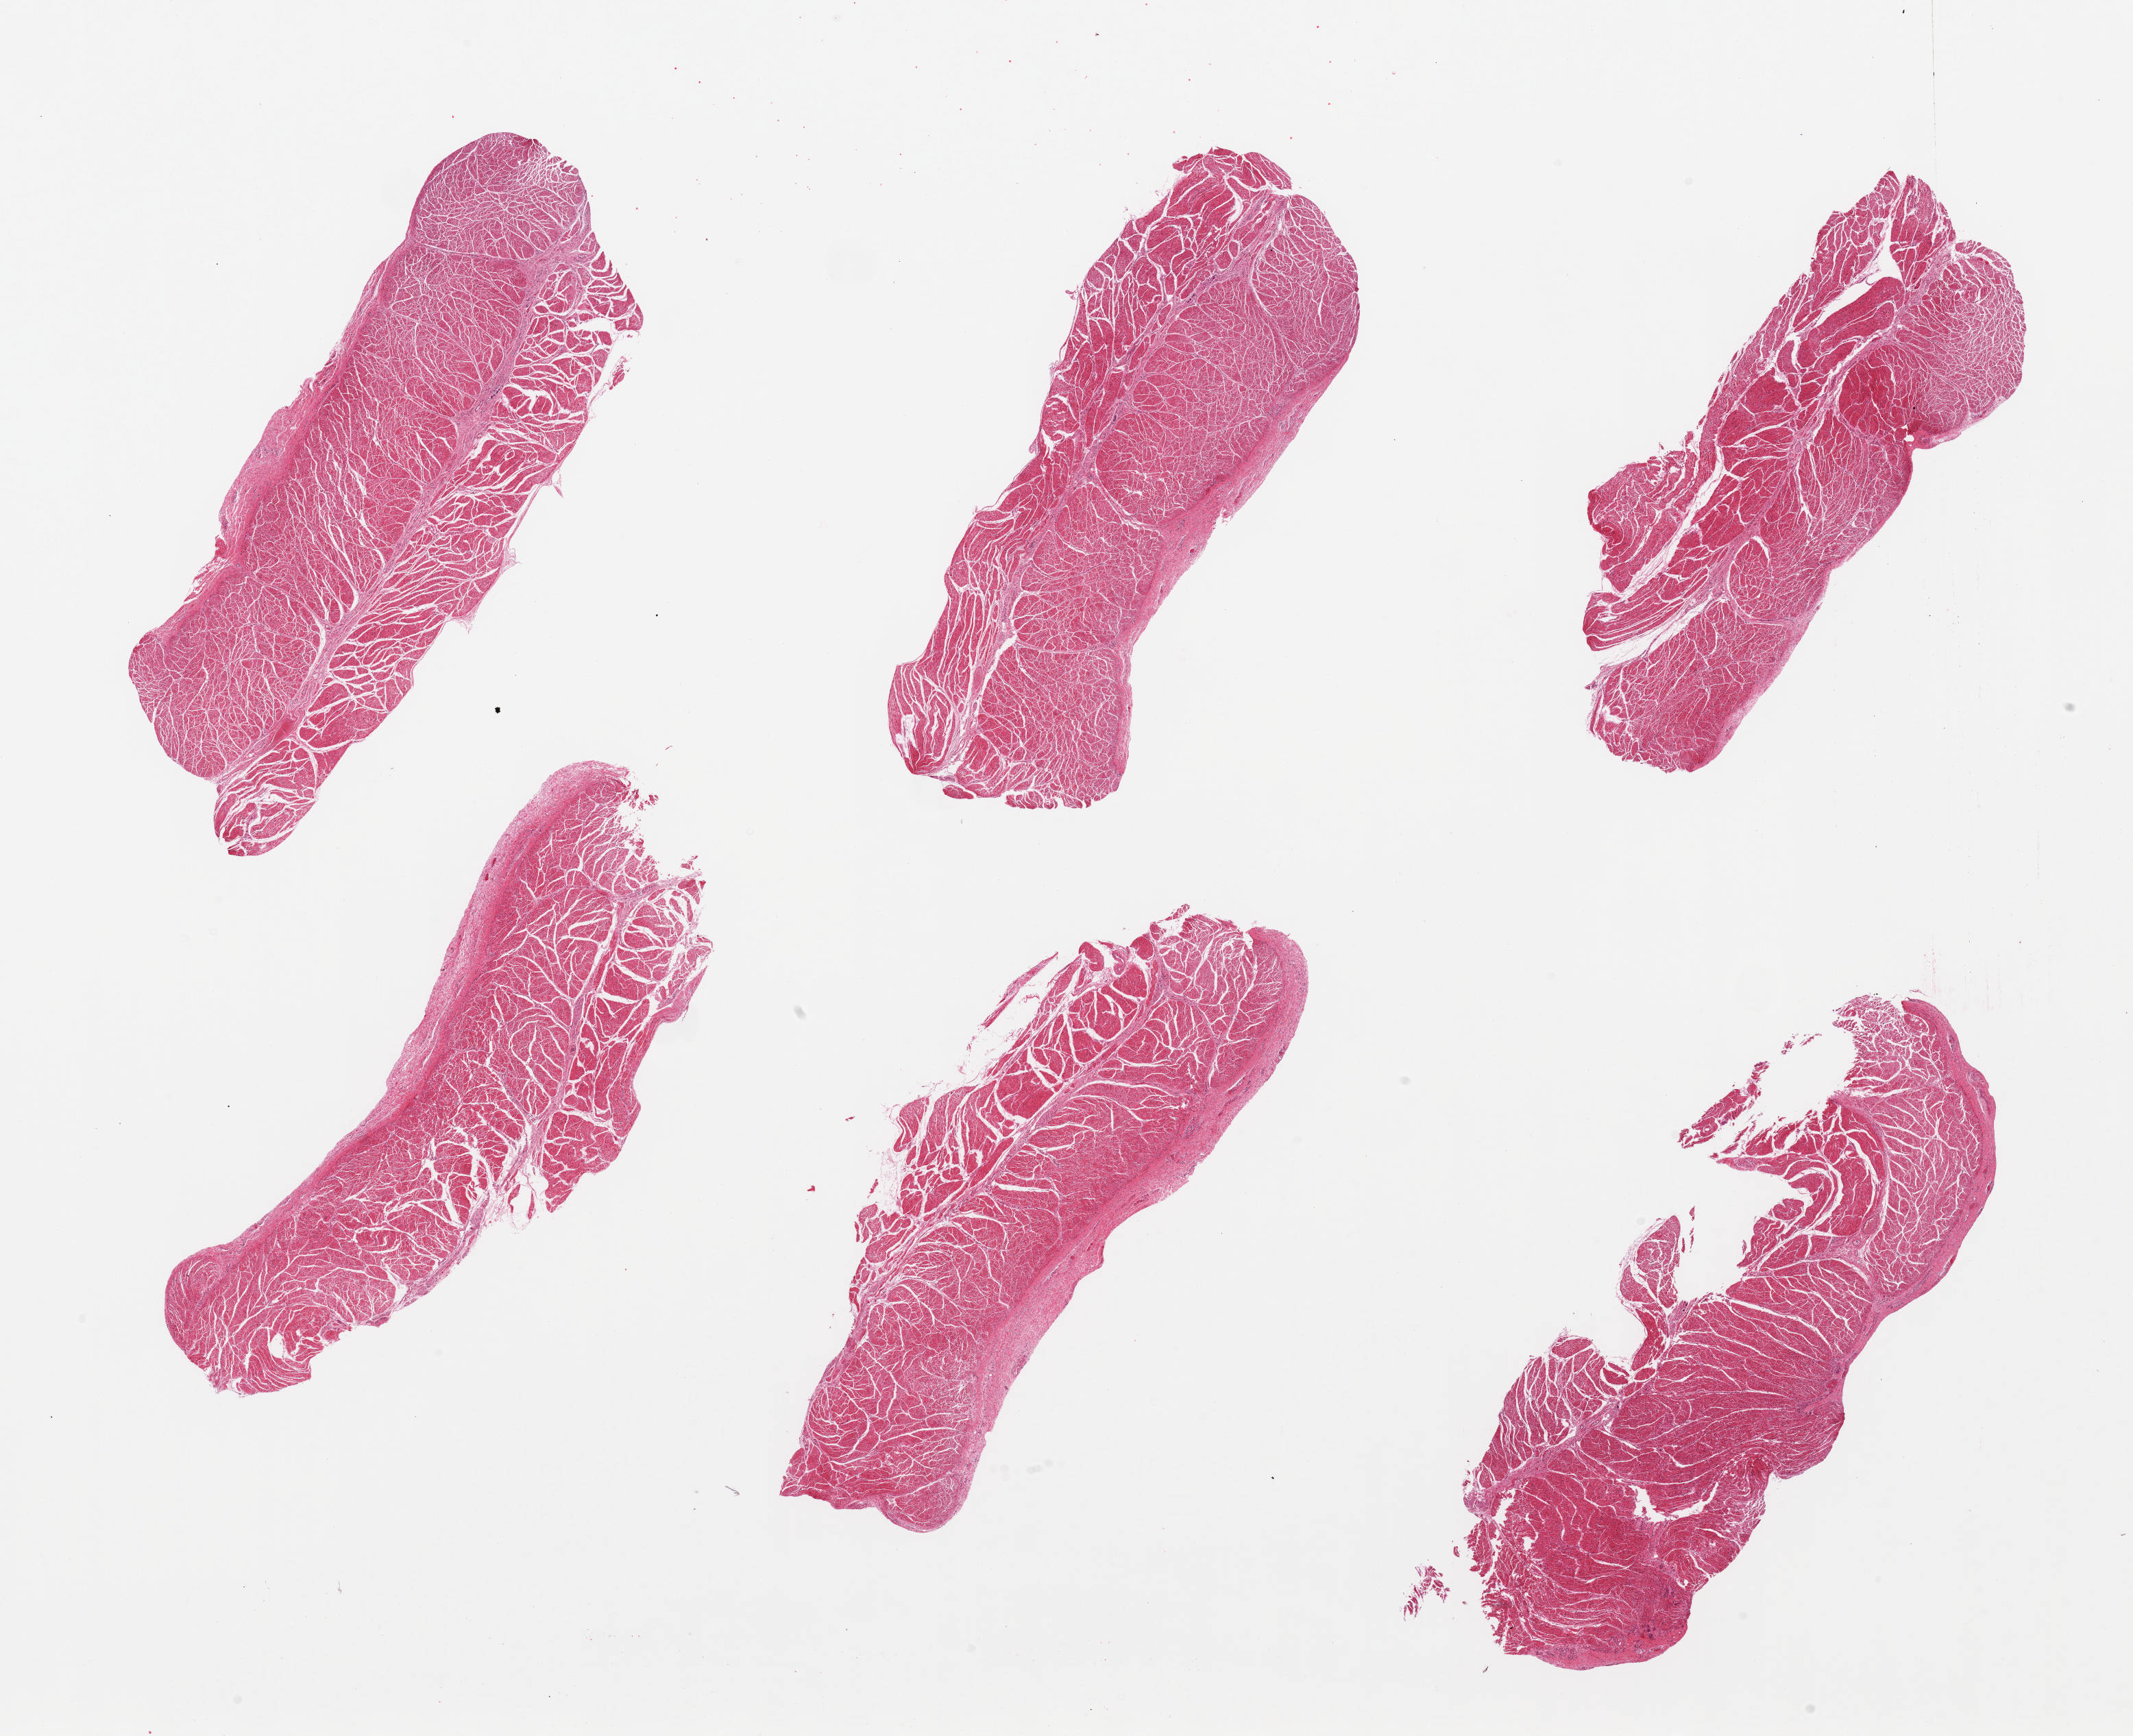
Haematoxylin and eosin whole-slide image, brightfield — low-resolution overview of the scanned area, about 24.6 x 20.0 mm (from a 20x scan); PAXgene-fixed, paraffin-embedded tissue; sampled site (target tissue): esophageal muscle; tissue donor sample.
* reviewer comment on this tissue sample: 6 pieces; well dissected muscle